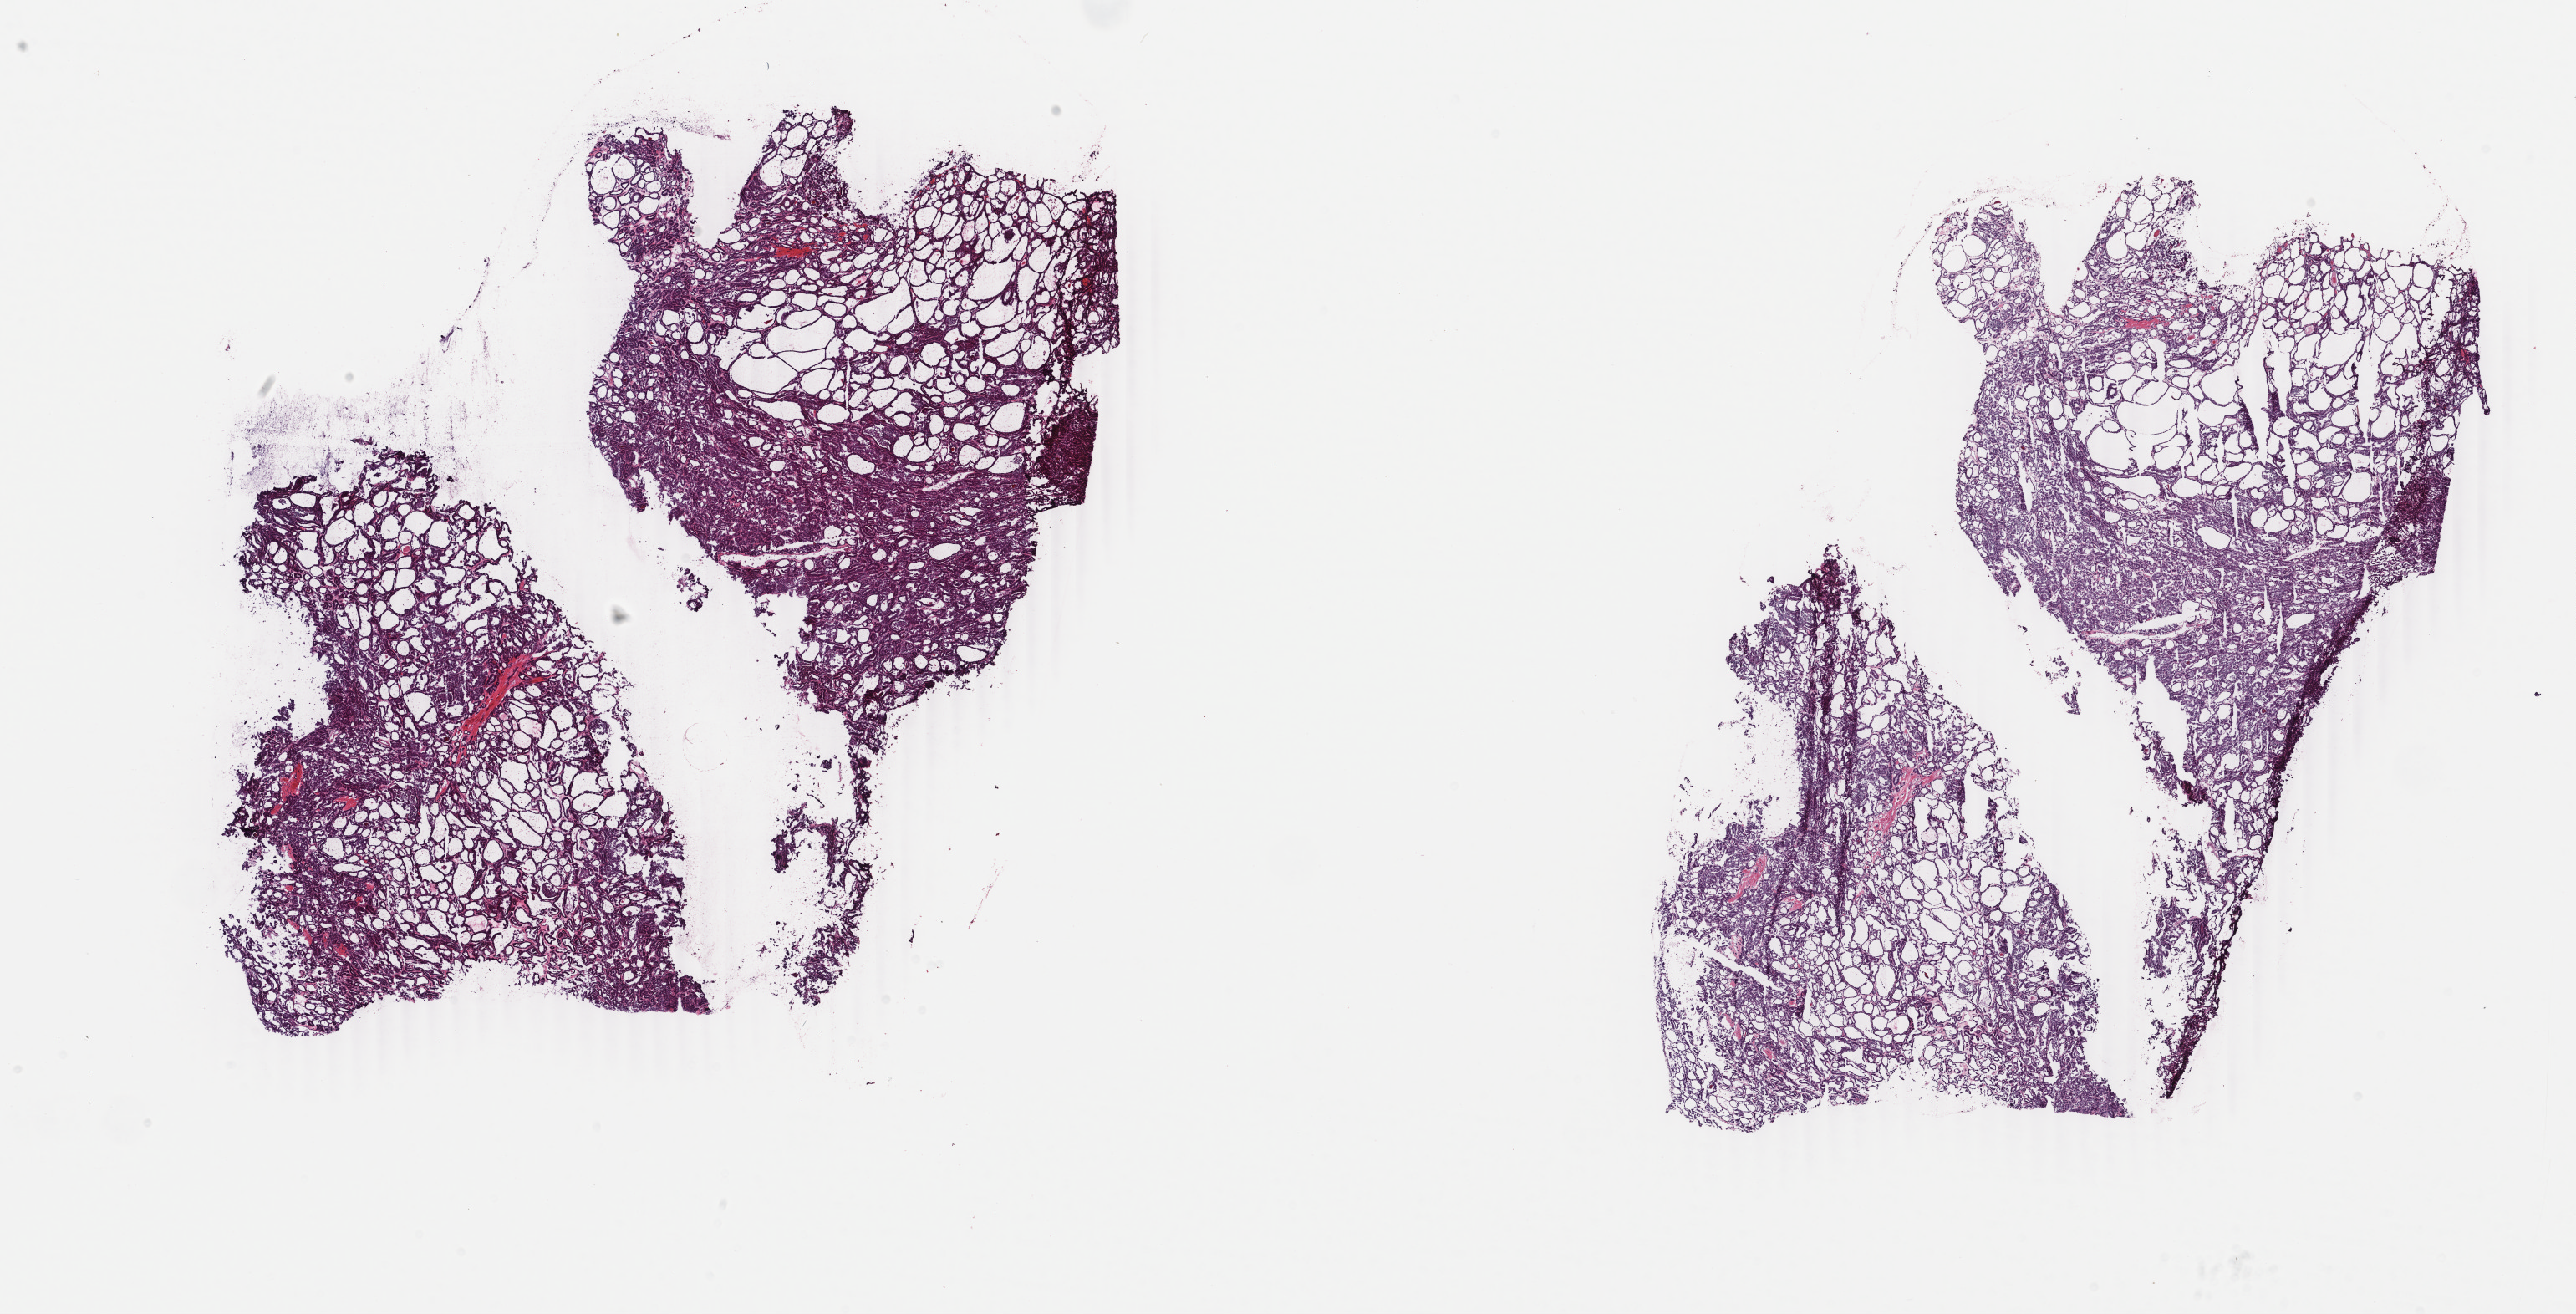
H&E-stained whole-slide image, whole scanned area (about 24.5 x 12.5 mm, acquisition: 40x scan) shown as a low-resolution overview, frozen section from the top of the tissue portion, thyroid, primary tumour sample. Patient: male, age at initial diagnosis 50 years. Composition of this section per pathologist review: tumour cells 100%, tumour nuclei 95%, normal cells 0%, stromal cells 0%, necrosis 0%. Infiltration values recorded for this section: lymphocyte infiltration 0%, monocyte infiltration 0%, neutrophil infiltration 0%.
AJCC pathologic stage: III (7th edition). Lymph nodes positive (case pathology): 0 of 2 examined. Pathologic diagnosis: Papillary carcinoma, follicular variant (thyroid gland). Laterality: right.